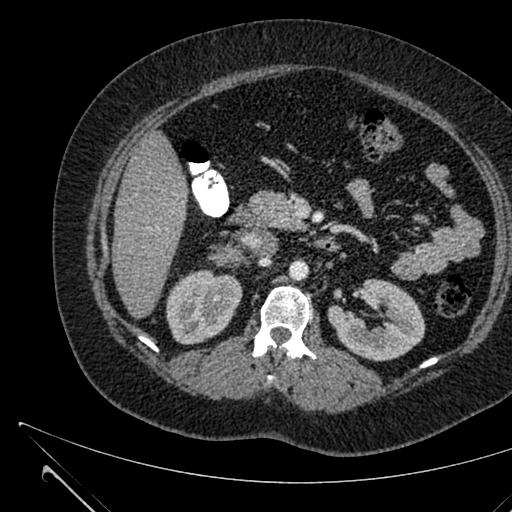
Contrast-enhanced abdominal CT, one axial slice; soft-tissue window (W 400 / L 40 HU); 512 × 512 image matrix. Female patient, age 36 years. Case-level facts recorded for this patient, not image findings: diagnosis: adrenocortical carcinoma; tumour side: right adrenal; tumour size at pathology: 10 cm; Ki-67 index: 20 %; stage (as recorded): 4.
Structures marked on this image (semi-automatically segmented with operator editing):
- mass: bounding box <216,246,240,263> (left, top, right, bottom; pixels)